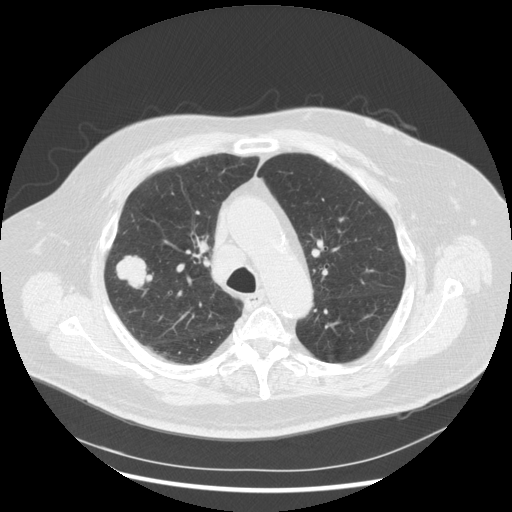
Low-dose screening chest CT, axial slice, third screening round (two years after baseline), lung window (W 1500 / L -600 HU), 2.5 mm slice thickness, slice 195 of 263 in the series. Male participant, aged 72 years at enrolment. Former smoker at enrolment.
• Expert-annotated lung lesion, box from (x=104, y=250) to (x=159, y=299) px.
• The exam's reader record, not a measurement of the box and not confirmed to be the same lesion: non-calcified nodule or mass ≥4 mm, right upper lobe, 31 × 31 mm, poorly defined margins, soft tissue attenuation, pre-existing on the prior screen: no.
• Official screen result: positive, other.
• Lung cancer was diagnosed 70 days after this screen: squamous cell carcinoma, NOS, right upper lobe, poorly differentiated (G3), stage IIIA (AJCC 6th edition), 19 mm at pathology.